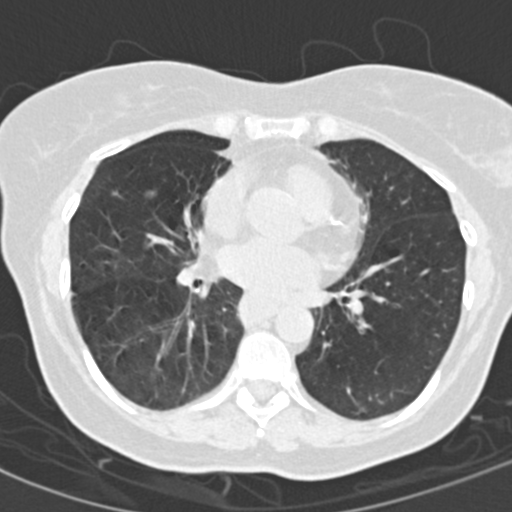
Low-dose screening chest CT, one axial slice. Slice 71 of 154 in the series (ordered by position). Reconstruction kernel B30f. 120 kVp. Lung window (W 1500 / L -600 HU). 512 × 512 image matrix.
Structures marked on this image (outlined manually by an expert reader):
- lesion 1 (nodule, middle lobe of right lung): bounding box [x1, y1, x2, y2] px = [144, 190, 157, 199]
- lesion 2 (nodule, middle lobe of right lung): [112, 189, 122, 197]